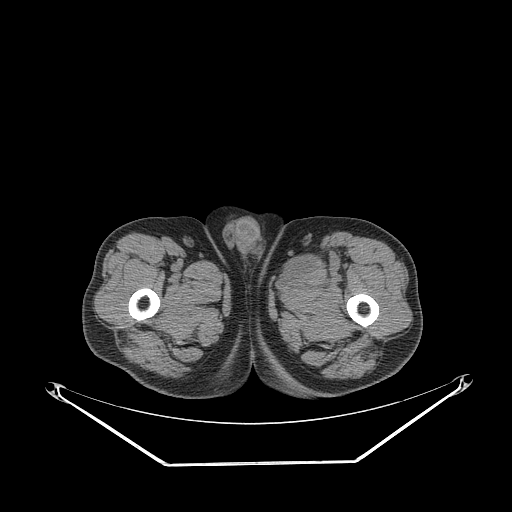
CT of an extremity soft-tissue mass (from a PET/CT study), one axial slice; position 266 of 267 along the scan axis; soft-tissue window (W 400 / L 40 HU); 3.75 mm slice thickness; 512 × 512 image matrix, field of view 500 × 500 mm. Male patient. Case-level facts recorded for this patient, not image findings: histological type: pleiomorphic liposarcoma; grade: high; site of the primary tumour: left thigh.
Annotated regions visible in this slice (expert contour drawn on MRI and transferred to this co-registered scan by the dataset authors):
- gross tumour volume including surrounding oedema: bounding box [x1, y1, x2, y2] px = [283, 246, 346, 284]
- gross tumour volume (mass): [283, 253, 321, 282]